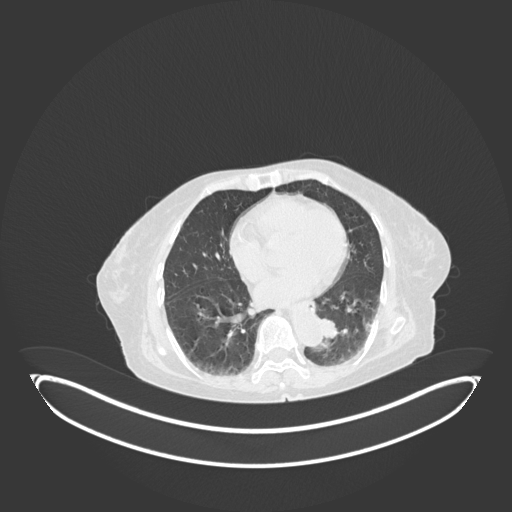
Chest CT, one axial slice; slice 36 of 189 in the series (ordered by position); 120 kVp; lung window (W 1500 / L -600 HU); 1 mm slice thickness; 512 × 512 image matrix. Female patient, age 82 years. From the clinical record (not read from this slice): clinical TNM (as recorded): T1b N0 M1.
Structures marked on this image (bounding box drawn by a radiologist):
- lung tumour (recorded histology: adenocarcinoma): bounding box (x1, y1, x2, y2) in pixels: (319, 314, 344, 342)